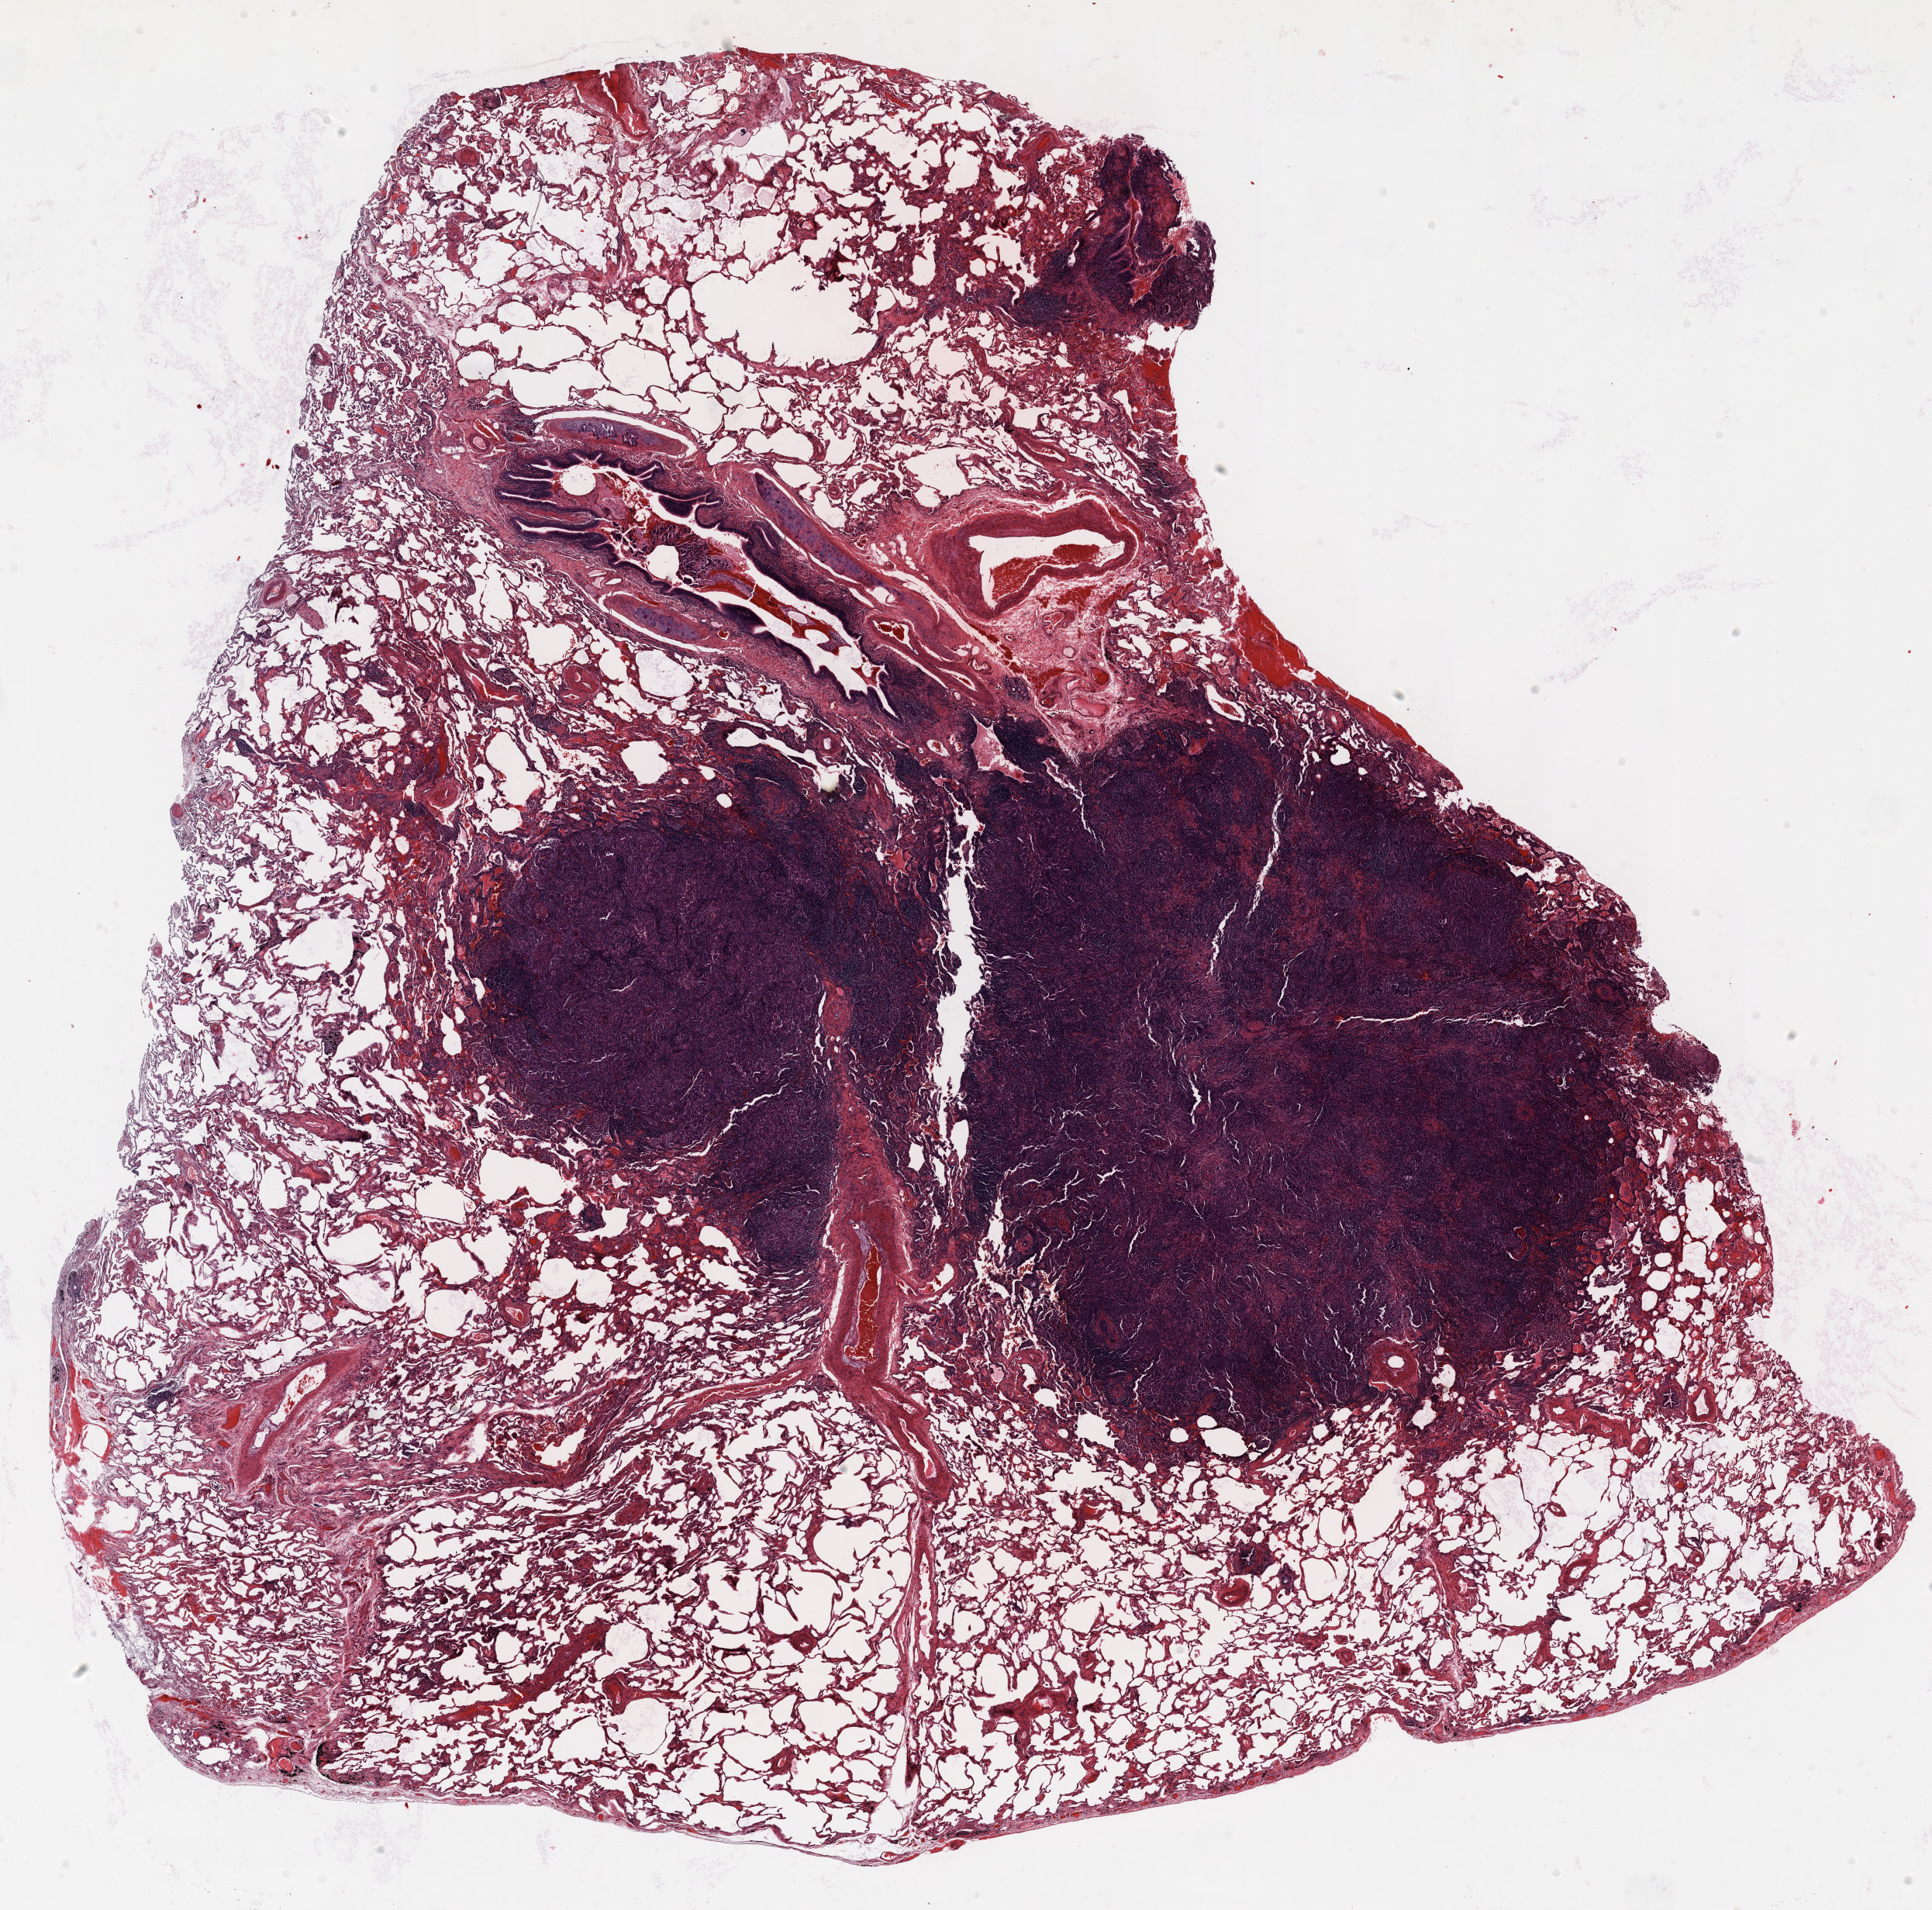
H&E whole-slide image — whole scanned area (about 20.0 x 19.8 mm, slide scanned at 20x) shown as a low-resolution overview. Formalin-fixed paraffin-embedded (FFPE) section. Lung. Female patient, aged 72 at enrolment. Former smoker at enrolment. Grade: moderately differentiated (G2).
Tumour size (pathology): 15 mm. Participant's lung-cancer diagnosis: Adenocarcinoma, NOS. Stage (AJCC 6th edition): IA. Primary tumour location (clinical record): right upper lobe. ICD-O-3 topography: upper lobe of lung (C34.1).